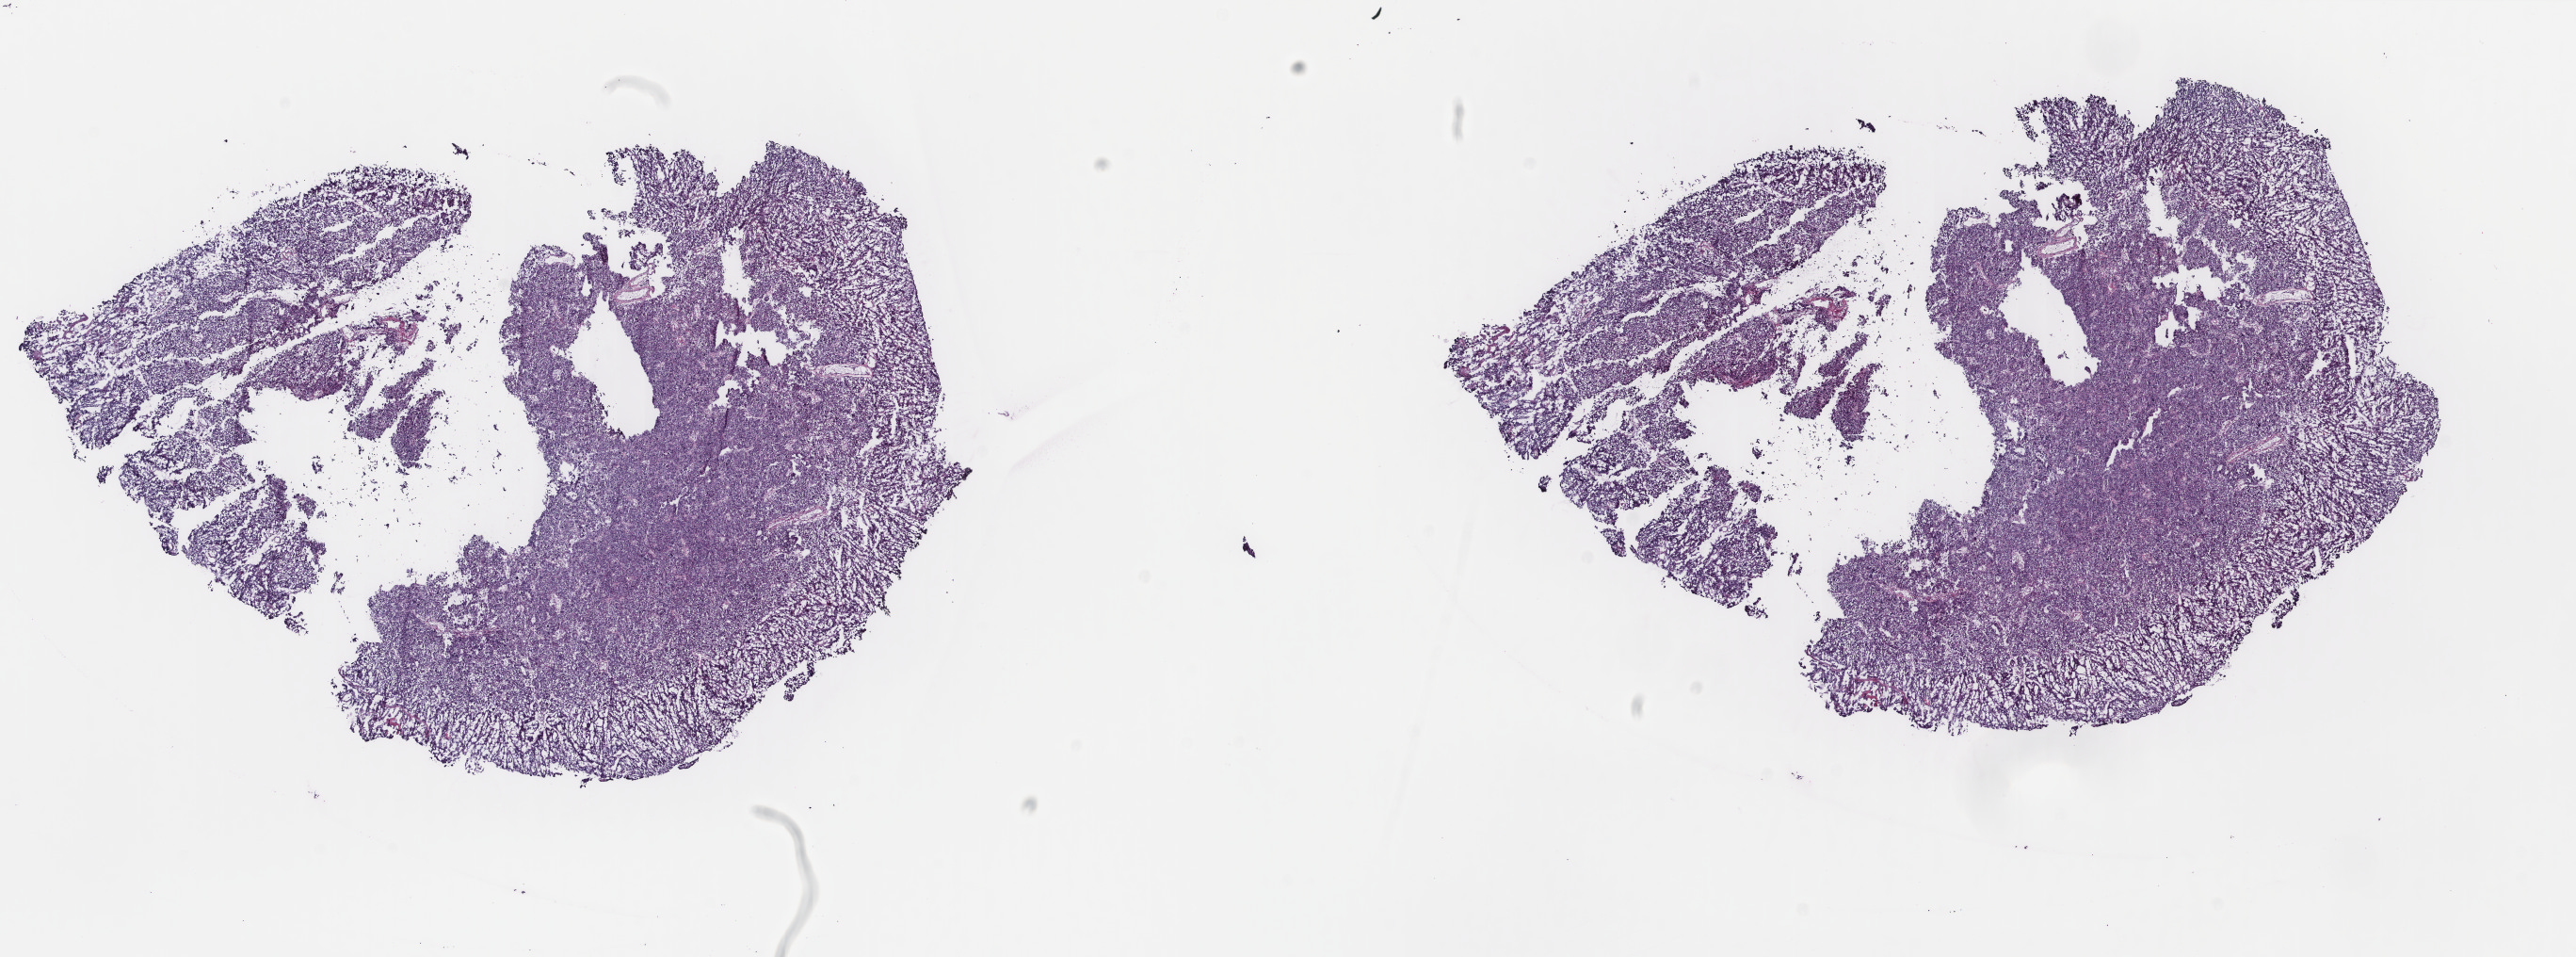
Digitized H&E-stained tissue section (whole slide), low-resolution overview of the scanned area, about 21.7 x 8.1 mm (acquisition: 40x scan), frozen section, primary tumour sample from the uterus. Patient: female, age at initial diagnosis 73 years. Histologic grade: G3 (poorly differentiated). Composition of this section per pathologist review: tumour cells 100%, tumour nuclei 95%, normal cells 0%, stromal cells 0%, necrosis 0%. Inflammatory infiltration, as recorded: lymphocyte infiltration 0%, monocyte infiltration 0%, neutrophil infiltration 0%.
* FIGO stage: IA
* lymph nodes positive (case pathology): 0 of 15 examined
* histologic diagnosis: Endometrioid adenocarcinoma, NOS